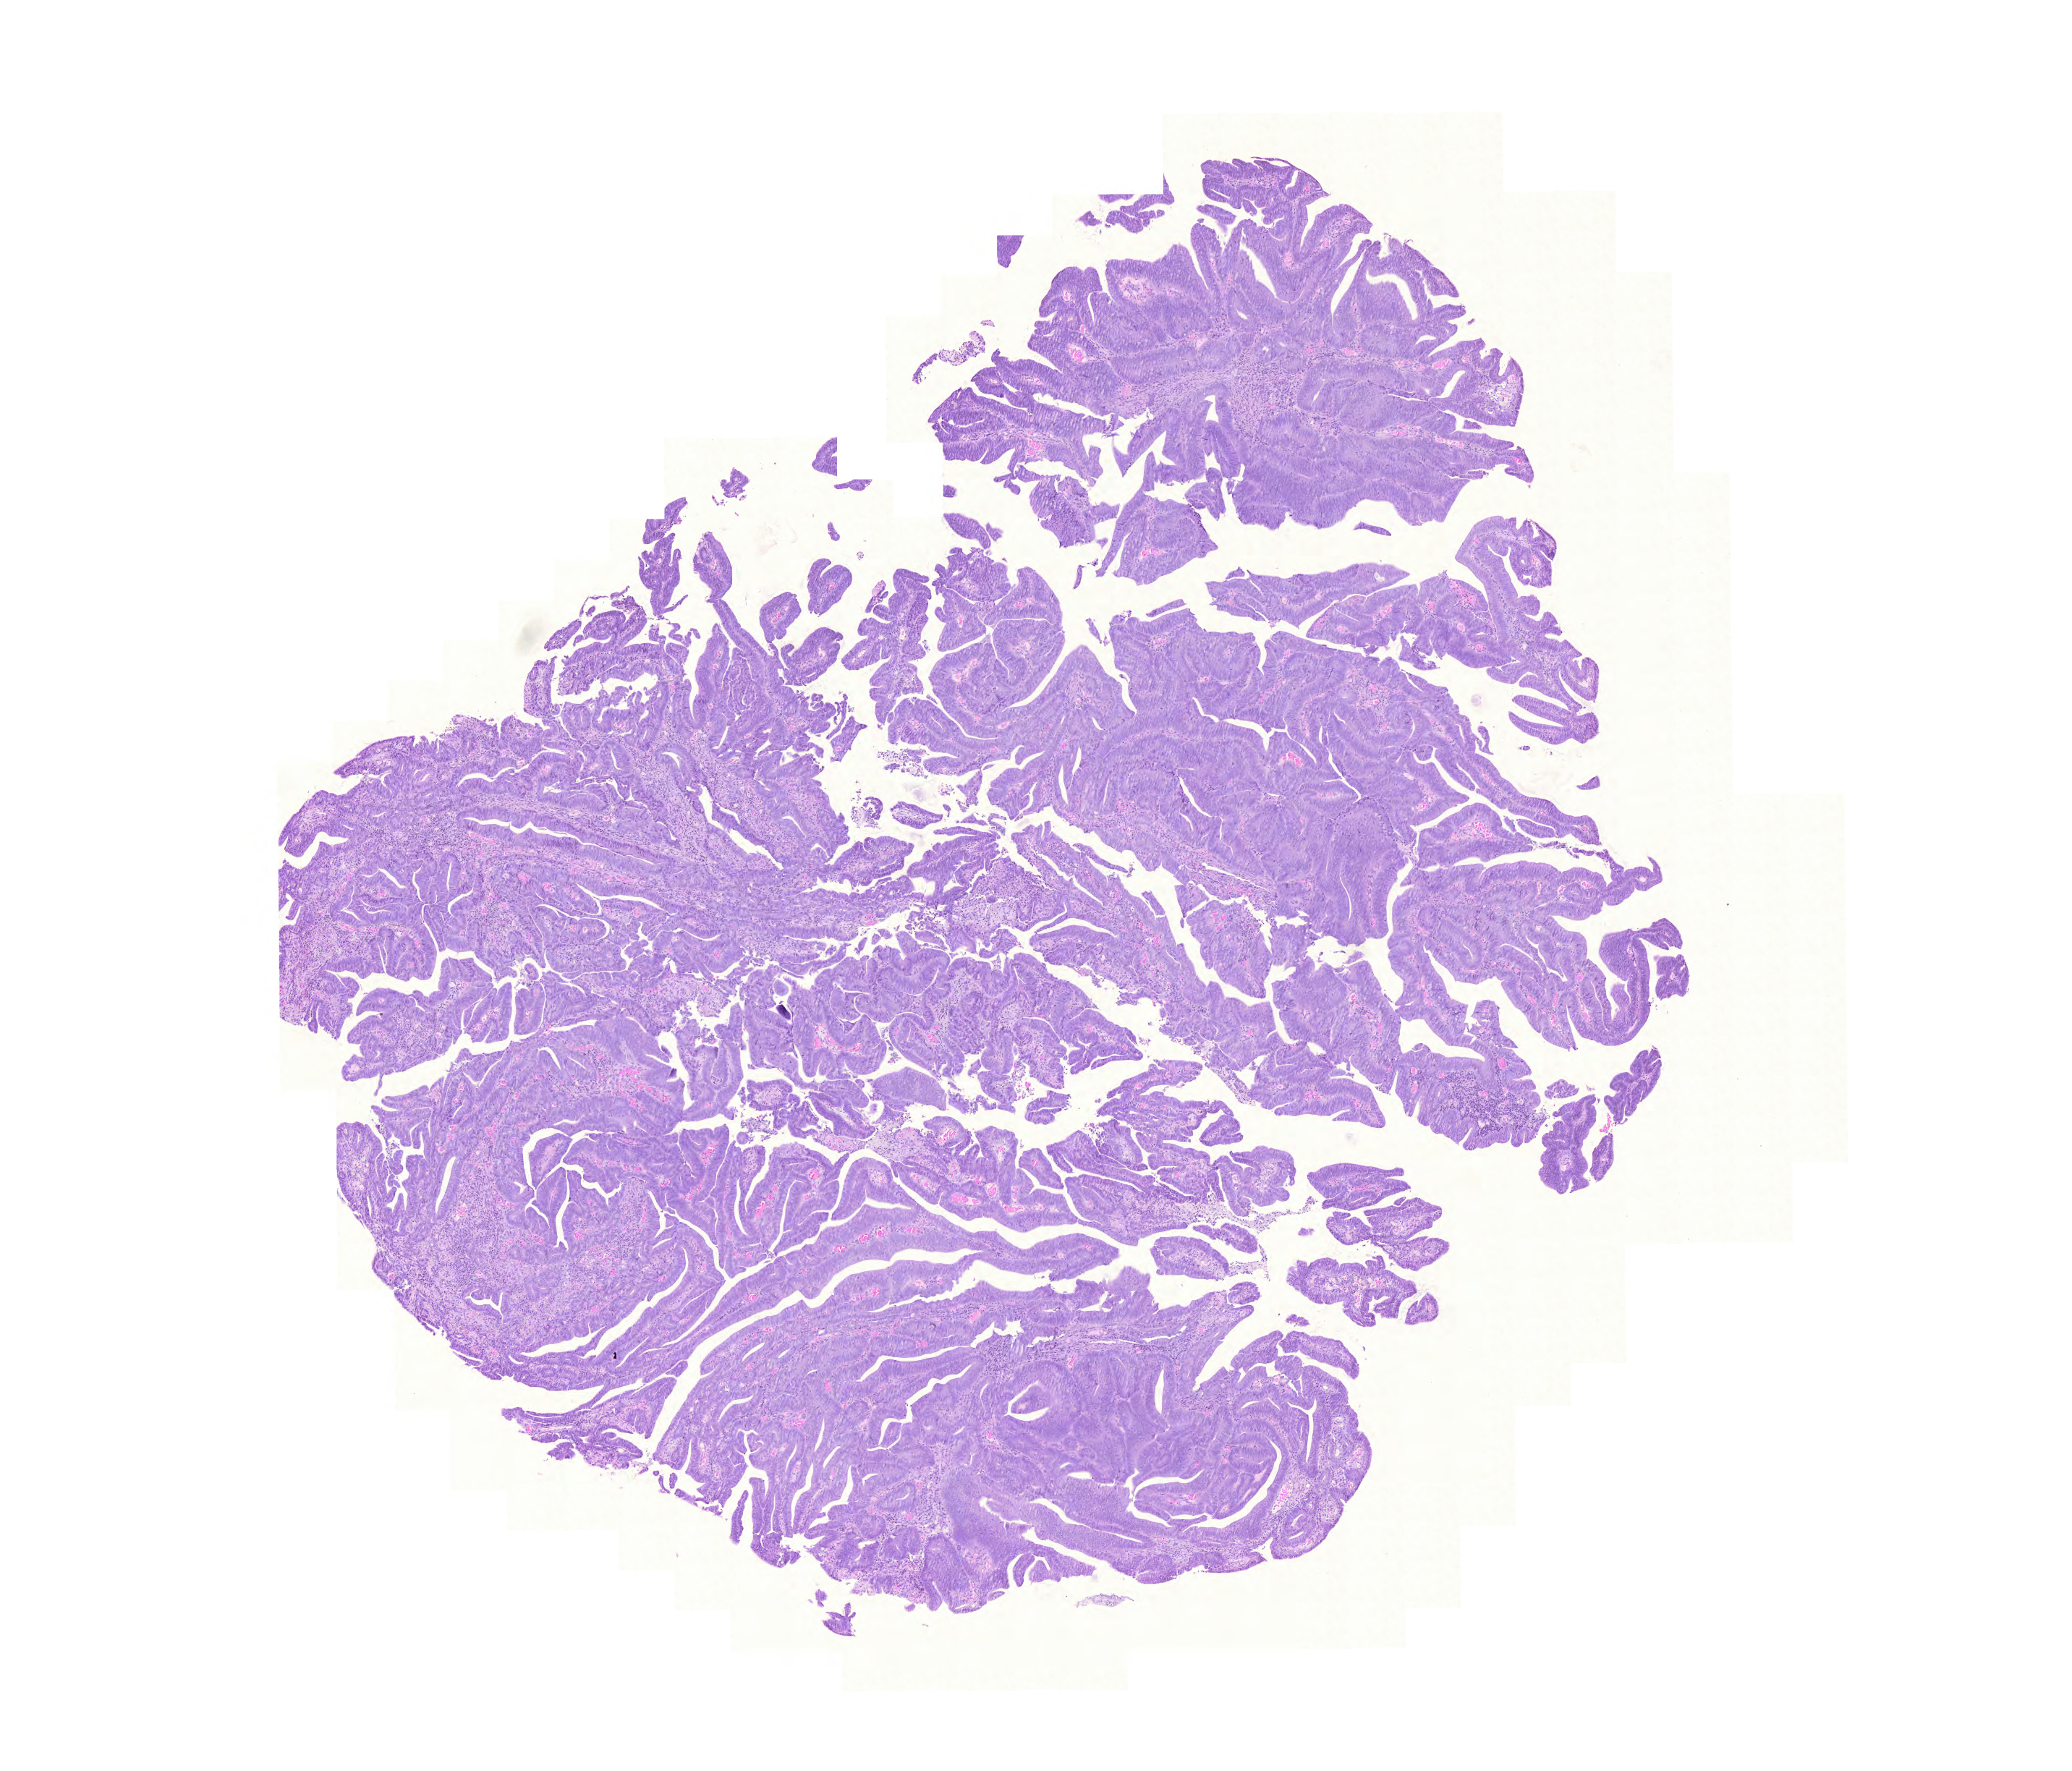
H&E whole-slide image, a low-resolution overview of the entire scanned area, about 10.7 x 9.1 mm, formalin-fixed paraffin-embedded (FFPE) diagnostic section, sample: primary tumour, colon. Patient: male, age at initial diagnosis 84 years.
Lymph nodes positive (case pathology): 0 of 24 examined. TNM: T3 N0 M0. Histologic diagnosis: Adenocarcinoma, NOS (ascending colon). AJCC pathologic stage: II (5th edition).